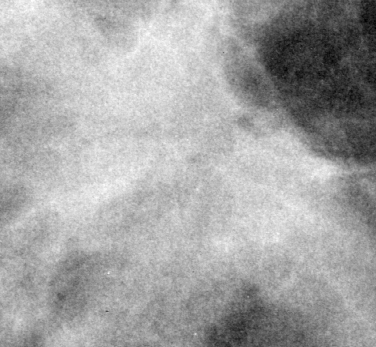
Region of interest cut from a scanned film mammogram (one marked finding); right breast; CC view.
Mass, shape irregular / architectural distortion, margins spiculated; BI-RADS assessment category 4; subtlety rating 2 on a 1 (subtle) to 5 (obvious) scale; pathology result (as recorded, not read from the image): malignant.